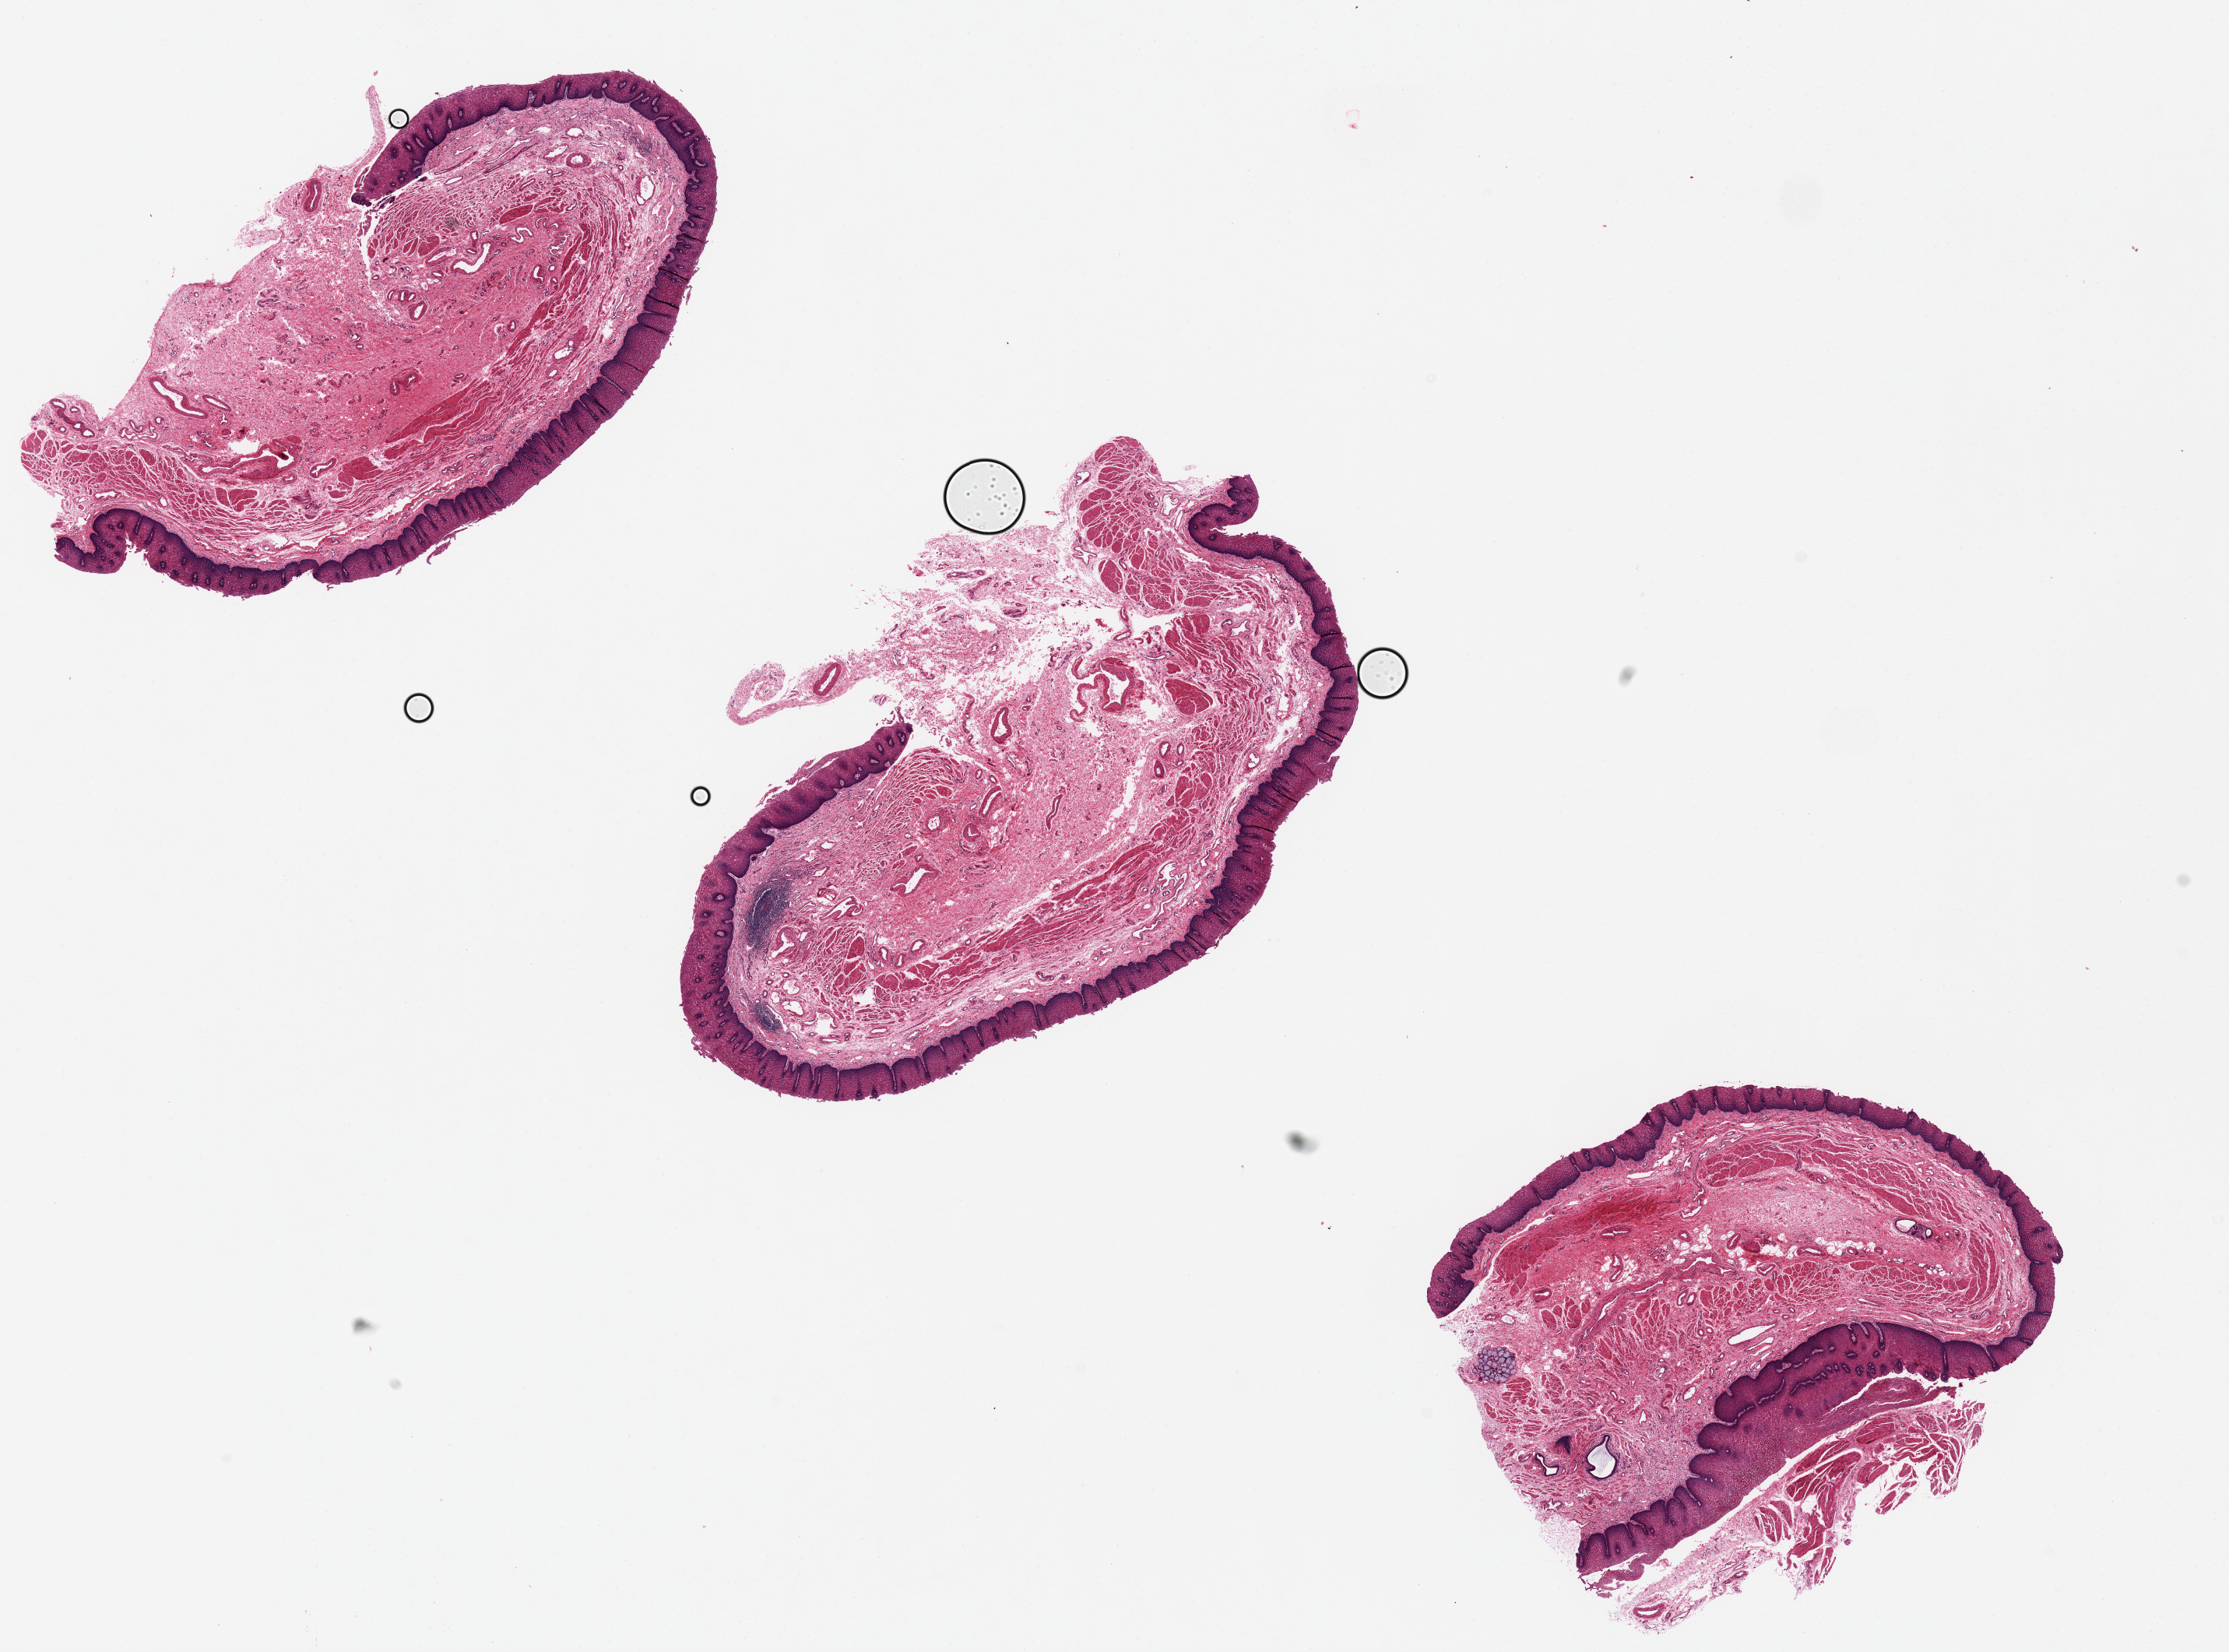
Hematoxylin and eosin (H&E) whole-slide image, brightfield, a low-resolution overview of the entire scanned area, about 22.6 x 16.8 mm (slide scanned at 20x). PAXgene-fixed paraffin-embedded (PFPE) section. Sampled site (target tissue): esophageal mucous membrane. Tissue donor sample.
• review note (as recorded): Epithelium is 10% of aliquot thickness